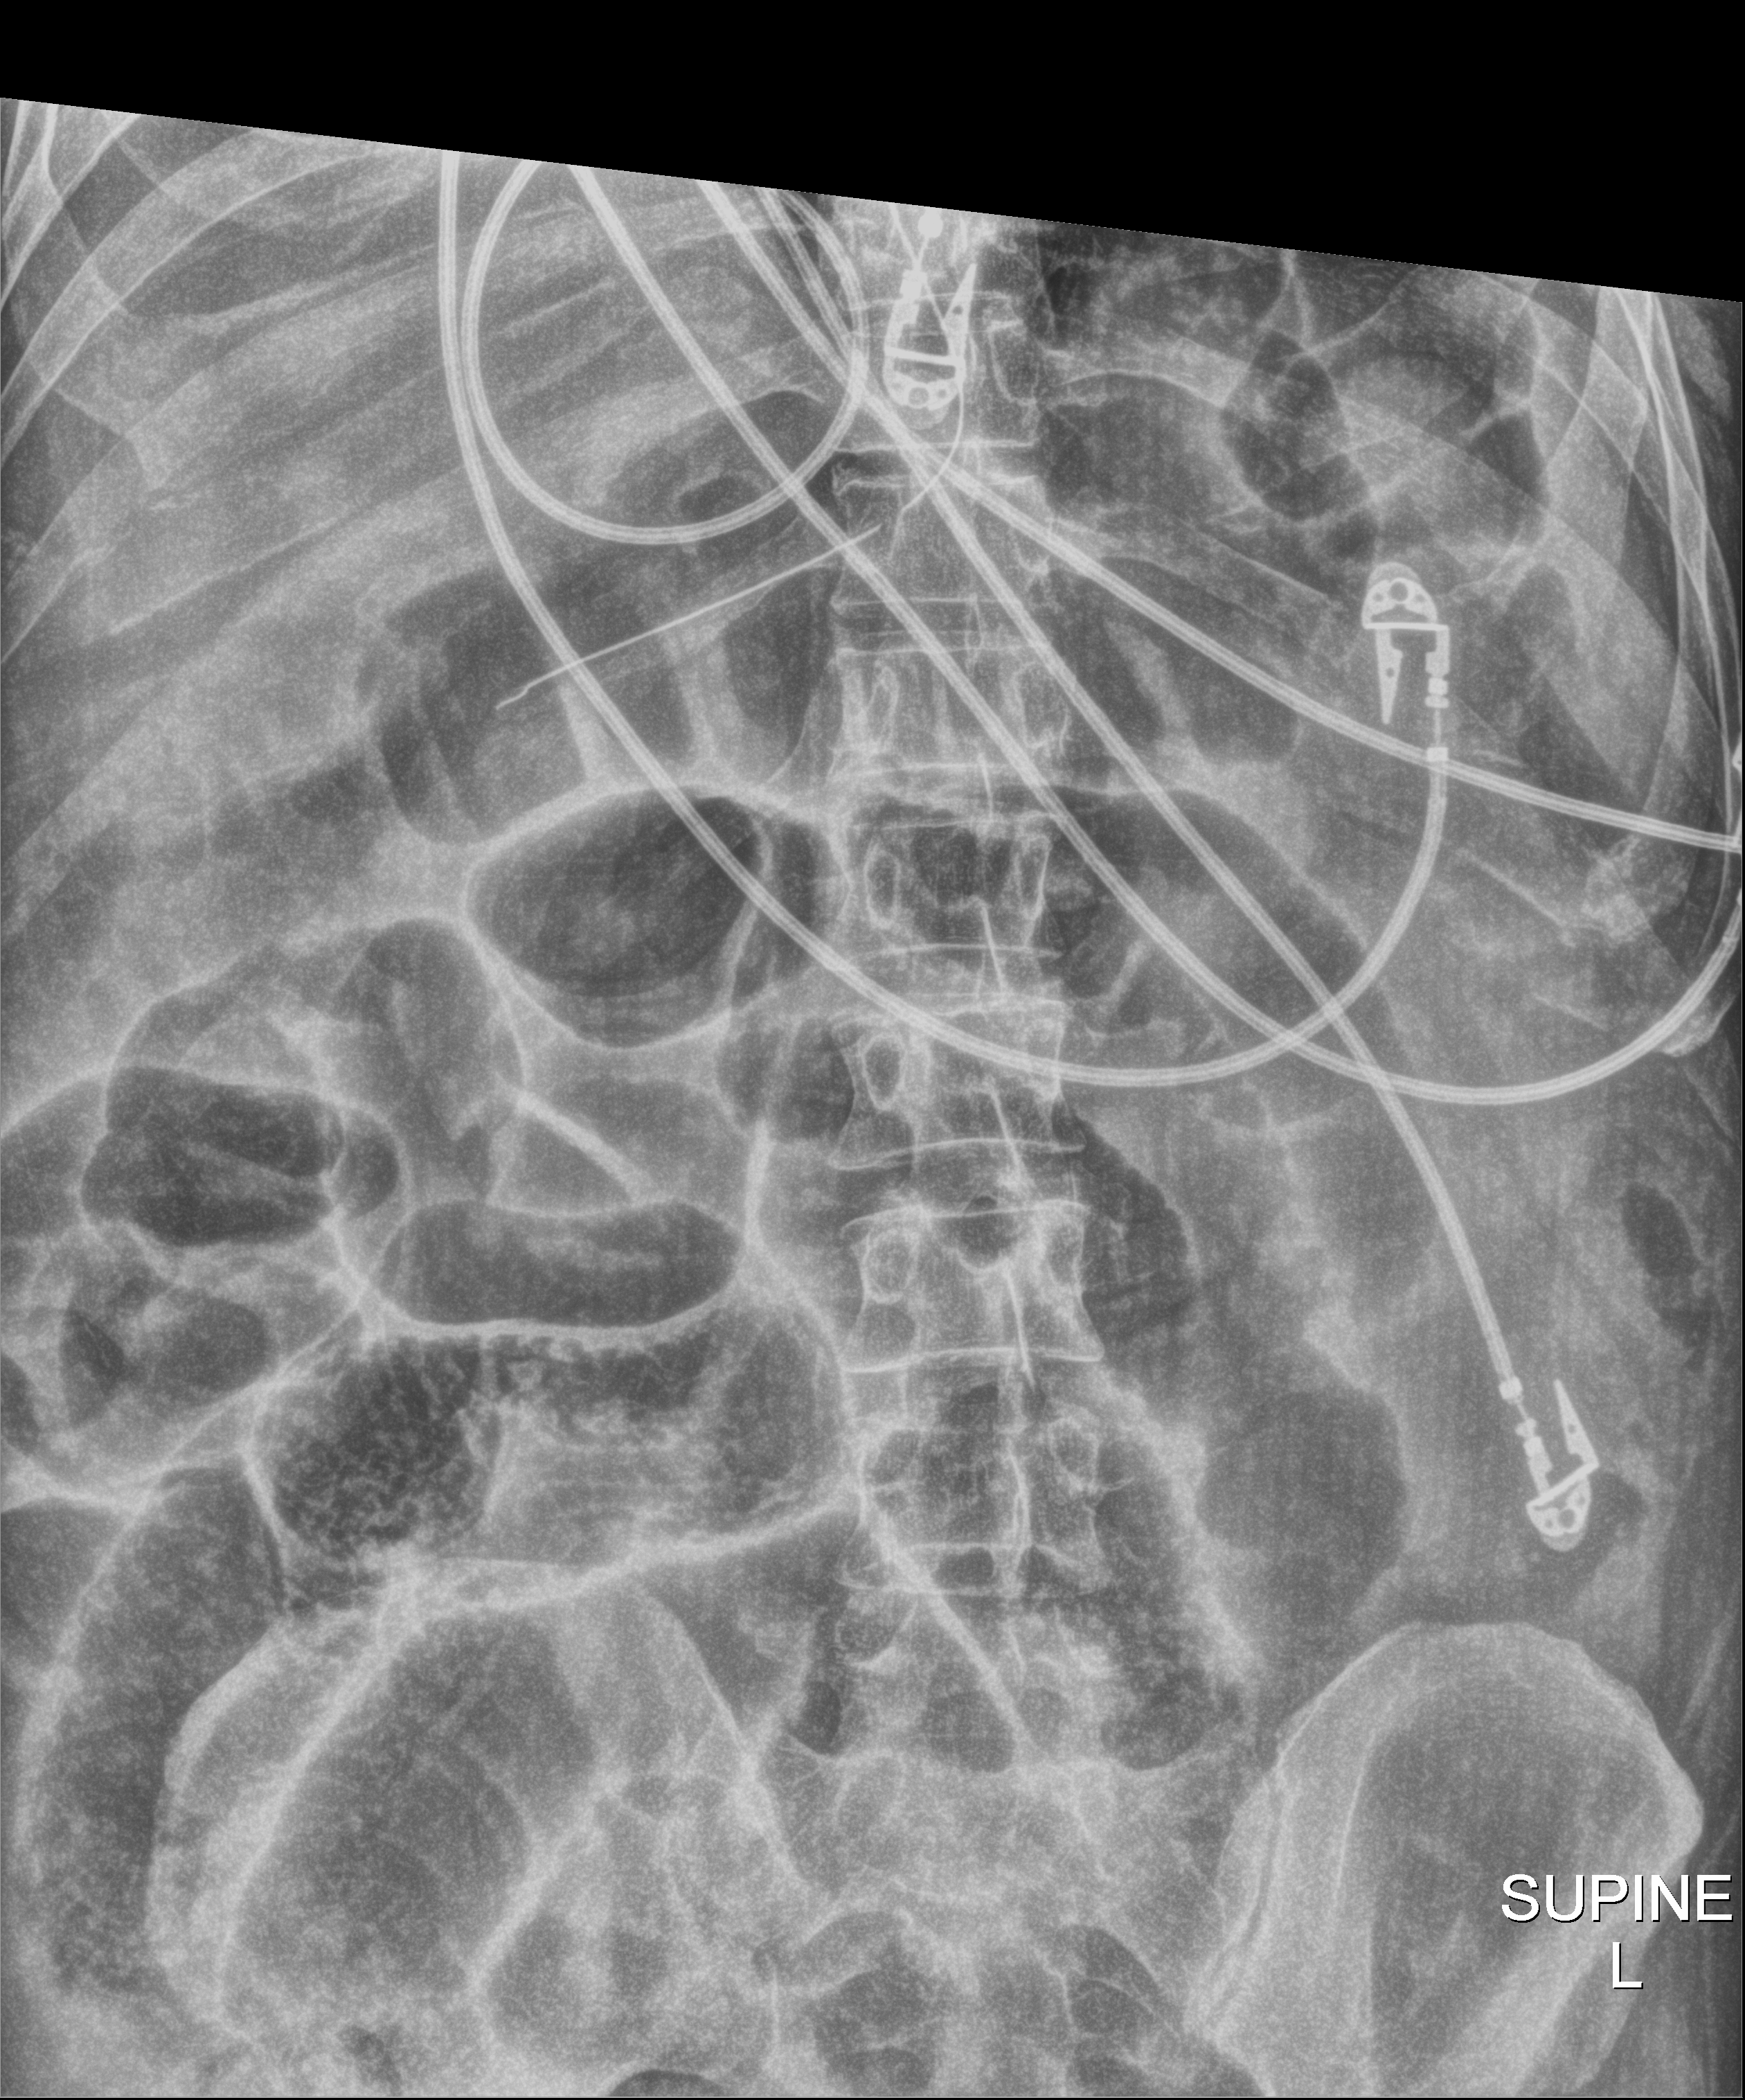
Abdomen X-ray (portable), anteroposterior (AP) projection. Adult patient hospitalised with COVID-19, age 18–59 years.
From the hospital-stay record, not from the radiograph (when in the stay this image was taken is not recorded):
- mechanically ventilated during this hospital stay: yes